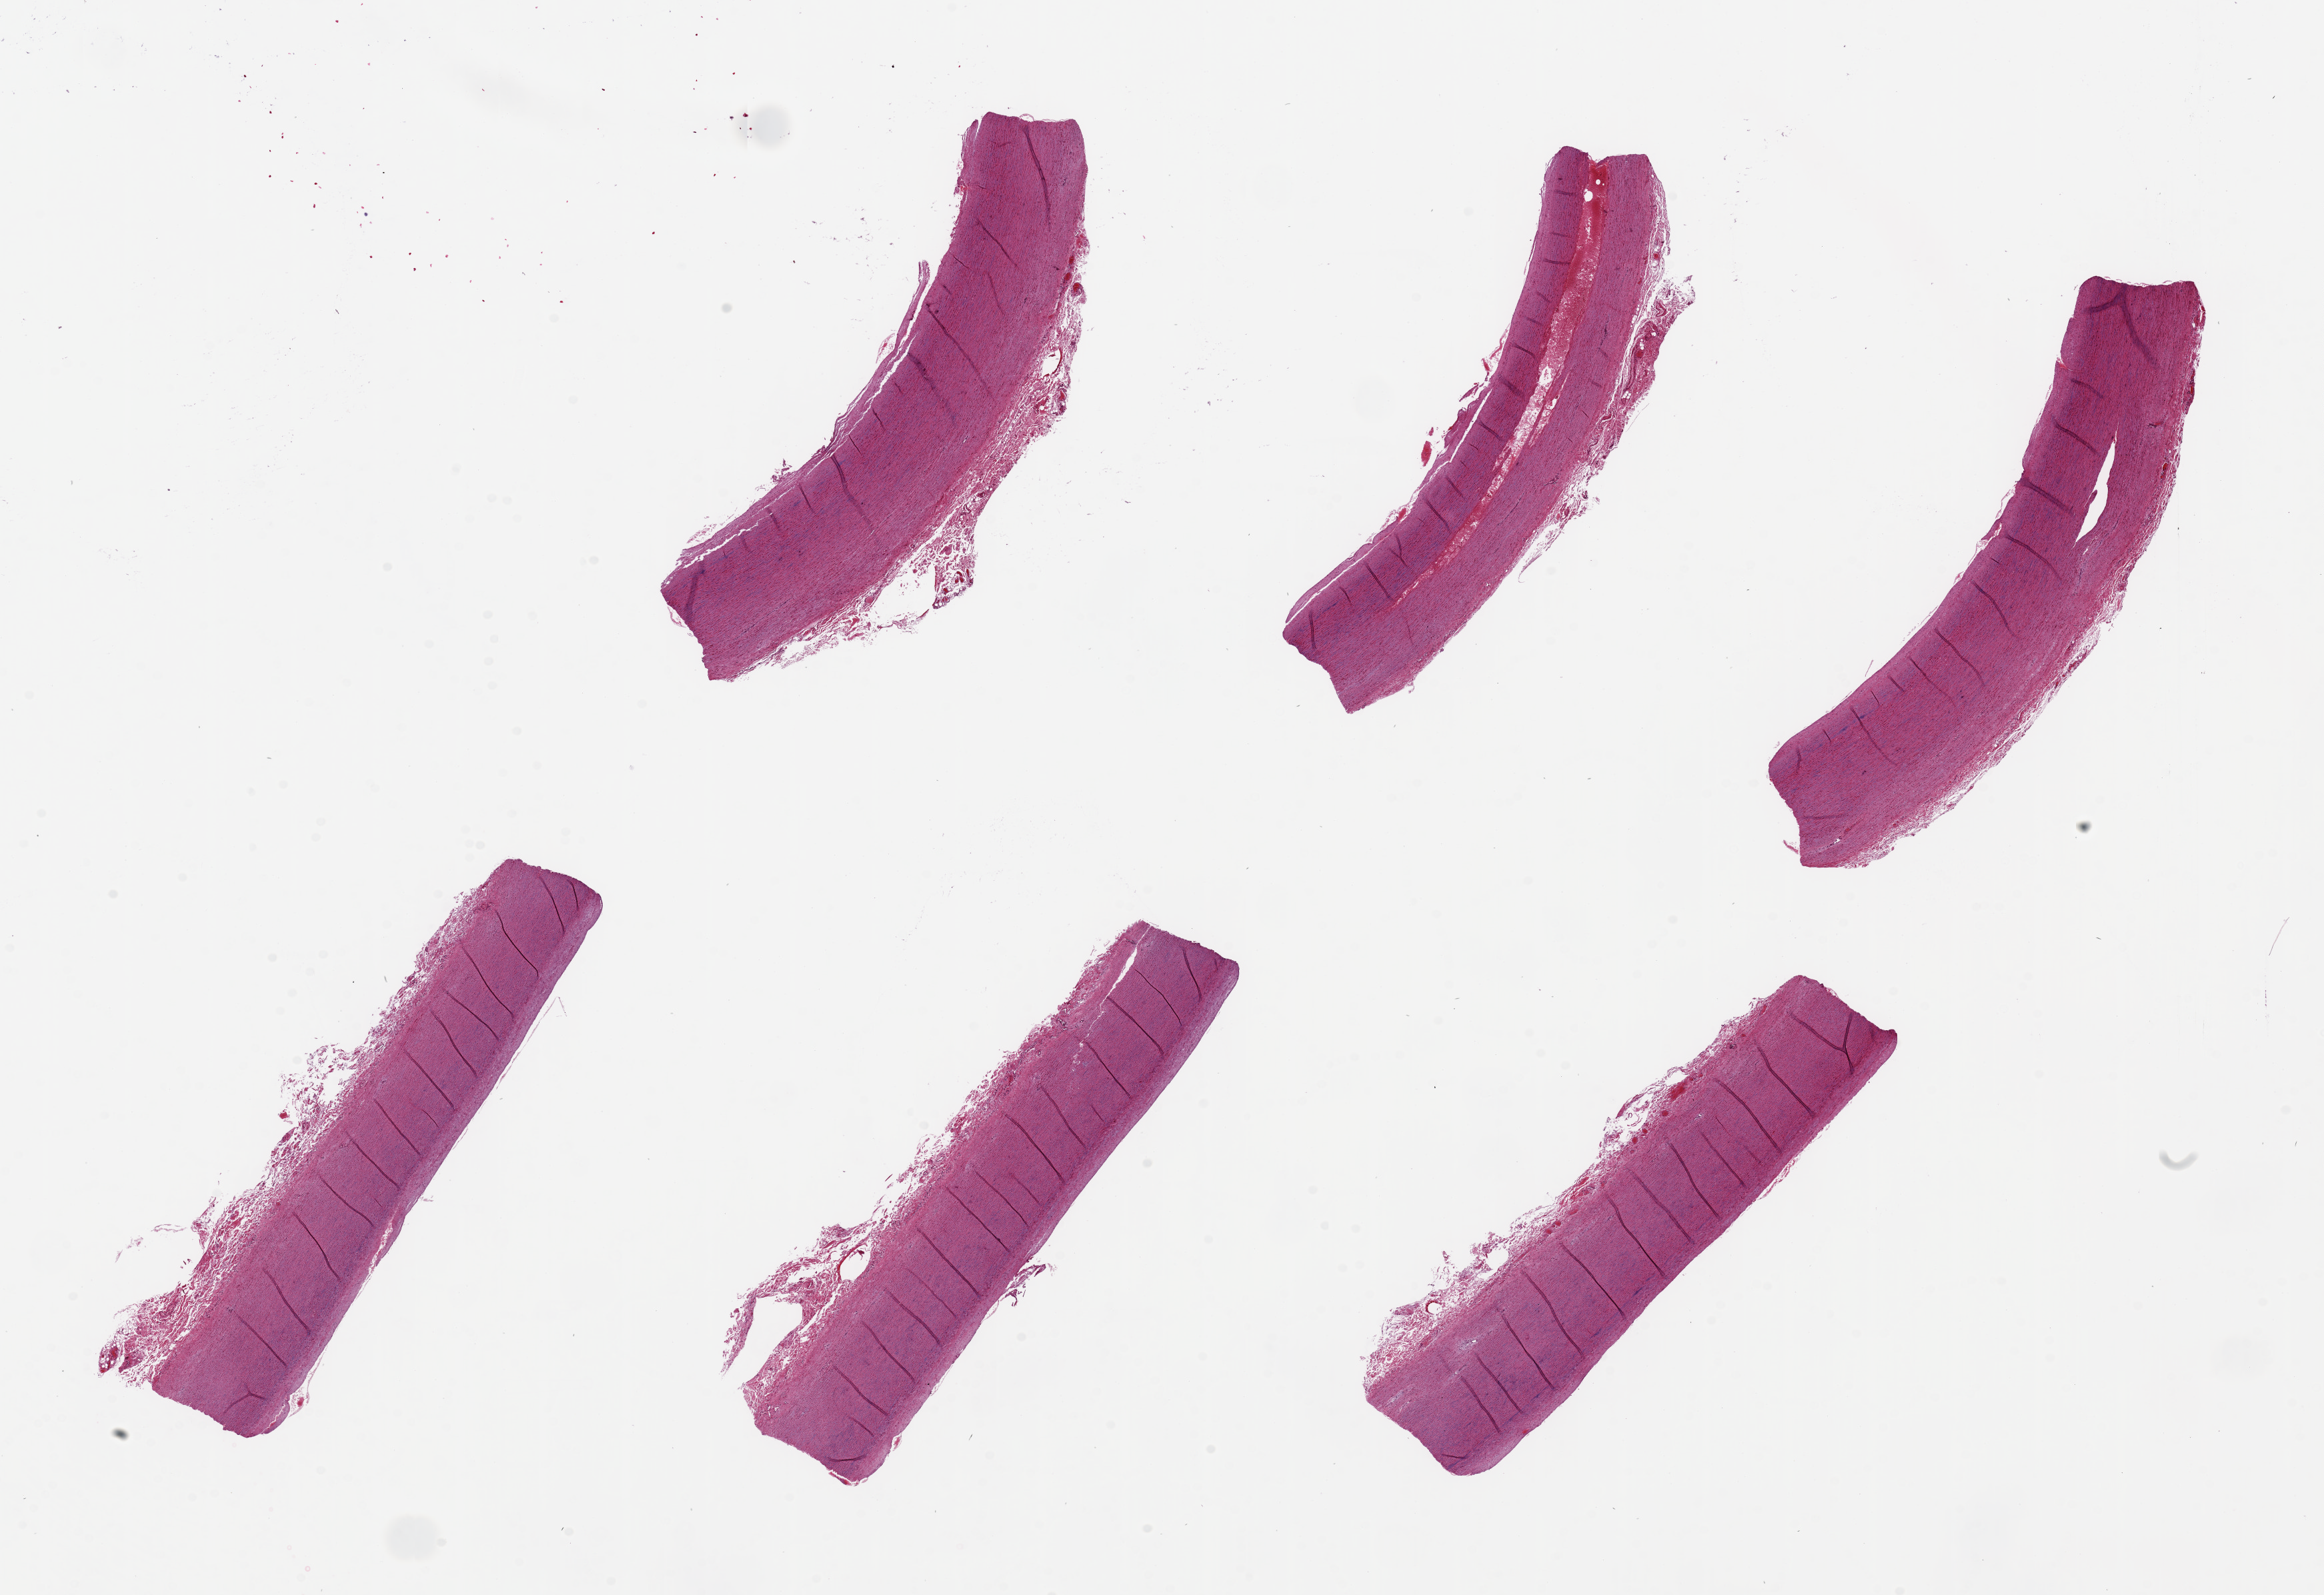
Whole-slide image, H&E stain, shown as a low-resolution overview of the whole scanned area (about 27.6 x 18.9 mm, from a 20x scan). PAXgene-fixed, paraffin-embedded tissue. Section of aorta (target tissue). Tissue donor sample. Female donor.
* pathologist's review note for this sample: 6 pieces ~8x1.5mm